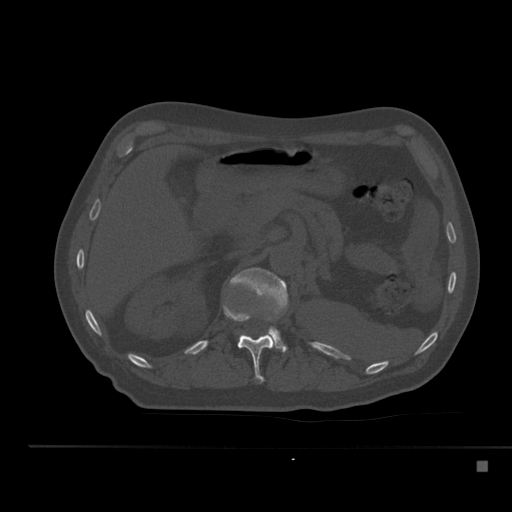
CT including the spine, one axial slice. Position 222 of 517 along the scan axis. Reconstruction kernel Br40s. Bone window (W 1800 / L 400 HU). 1.5 mm slice thickness. 512 × 512 image matrix, field of view 408 × 408 mm. Male patient, age 70 years. Case-level facts recorded for this patient, not image findings: primary cancer: renal.
Structures marked on this image (semi-automatically segmented with operator editing):
- L1 vertebra: bounding box [x1, y1, x2, y2] px = [230, 267, 288, 352]
- T12 vertebra: [223, 303, 275, 383]